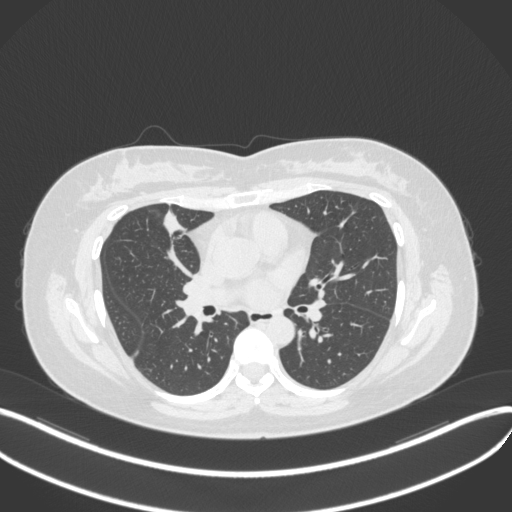
Chest CT, one axial slice. Position 167 of 272 along the scan axis. Reconstruction kernel B31f. Lung window (W 1500 / L -600 HU). 1 mm slice thickness. 512 × 512 image matrix. Female patient, age 42 years. From the clinical record (not read from this slice): clinical TNM (as recorded): T1b N0 M0.
Annotated regions visible in this slice (rectangle marked by the reading radiologist):
- lung tumour (recorded histology: adenocarcinoma): bounding box <159,203,188,243> (left, top, right, bottom; pixels)